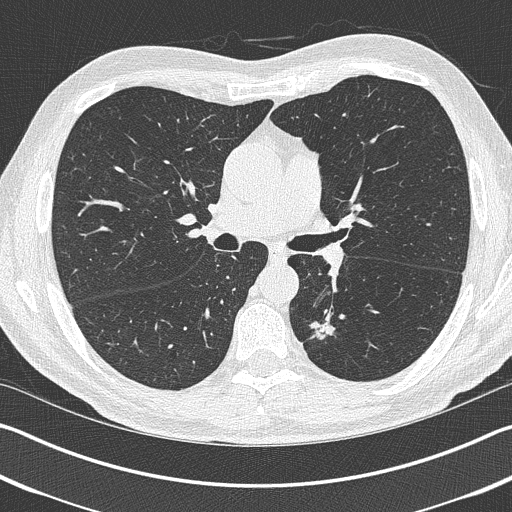
Low-dose screening chest CT, one axial slice; position 245 of 402 along the scan axis; 120 kVp; lung window (W 1500 / L -600 HU); 1 mm slice thickness; 512 × 512 image matrix, field of view 340 × 340 mm.
Structures marked on this image (expert manual segmentation):
- lesion 1 (tumor, lower lobe of left lung): box from (x=310, y=322) to (x=335, y=340) px